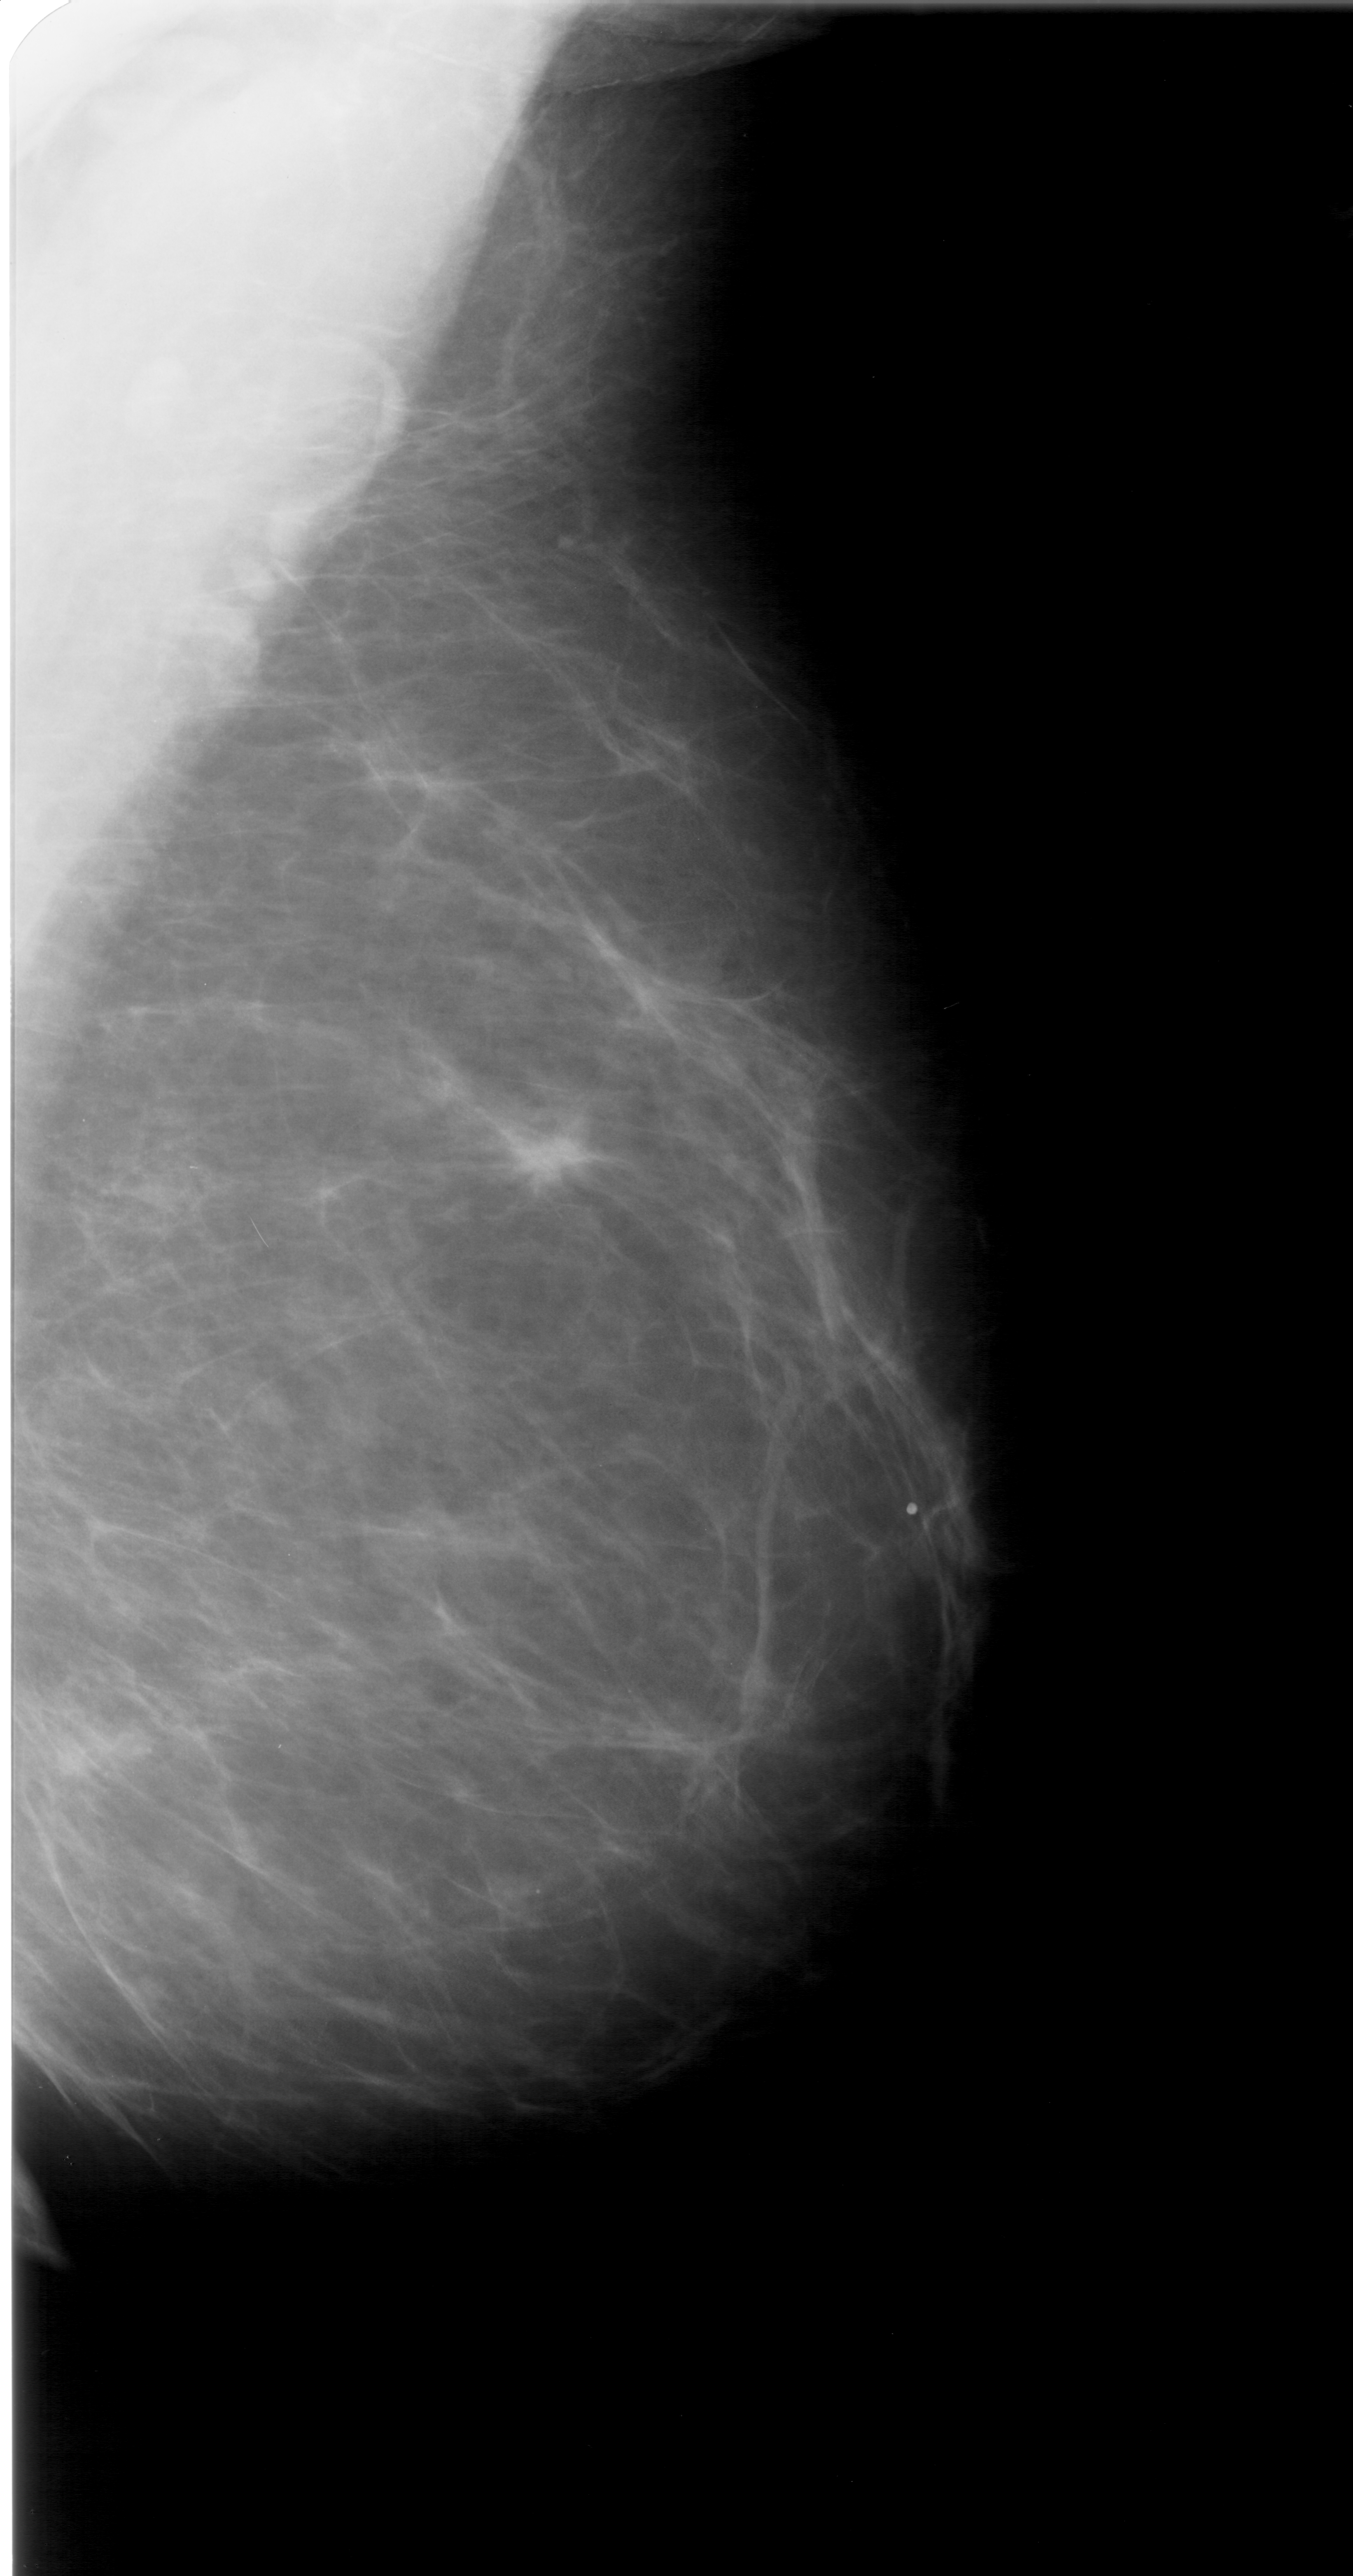
Scanned film-screen mammogram; right breast; MLO view.
Mass, shape irregular, margins spiculated; BI-RADS assessment category 5; subtlety rating 5 on a 1 (subtle) to 5 (obvious) scale; pathology (as recorded): malignant.